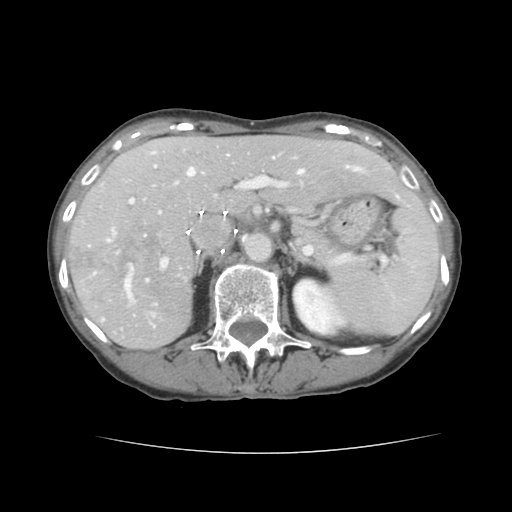
Contrast-enhanced abdominal CT, one axial slice. Slice 89 of 136 in the series (ordered by position). 120 kVp. Intravenous contrast given. Soft-tissue window (W 400 / L 40 HU). 2.5 mm slice thickness. 512 × 512 image matrix, field of view 319 × 319 mm. Female patient, age 77 years. From the clinical record (not read from this slice): diagnosis: colorectal cancer liver metastases, imaged before liver resection.
Outlined on this slice (outlined manually by an expert reader):
- hepatic veins: bounding box <152,152,361,327> (left, top, right, bottom; pixels)
- liver: <68,136,423,348>
- planned liver remnant (the part of the liver to remain after resection): <153,136,420,213>
- portal vein (with intrahepatic branches): <107,165,305,300>
- liver metastasis: <117,225,163,287>